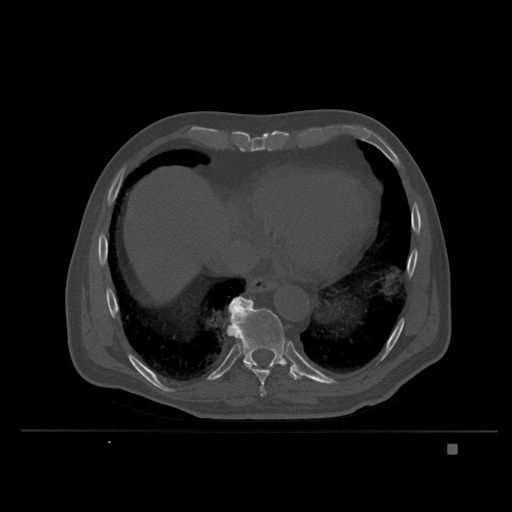
CT including the spine, one axial slice. Slice 203 of 435 in the series (ordered by position). Bone window (W 1800 / L 400 HU). 1.5 mm slice thickness. 512 × 512 image matrix, field of view 434 × 434 mm. Male patient, age 73 years. Case-level facts recorded for this patient, not image findings: primary cancer: skin.
Annotated regions visible in this slice (semi-automatically segmented with operator editing):
- T10 vertebra: box from (x=230, y=300) to (x=302, y=380) px
- T9 vertebra: (x=227, y=296)–(x=272, y=397)